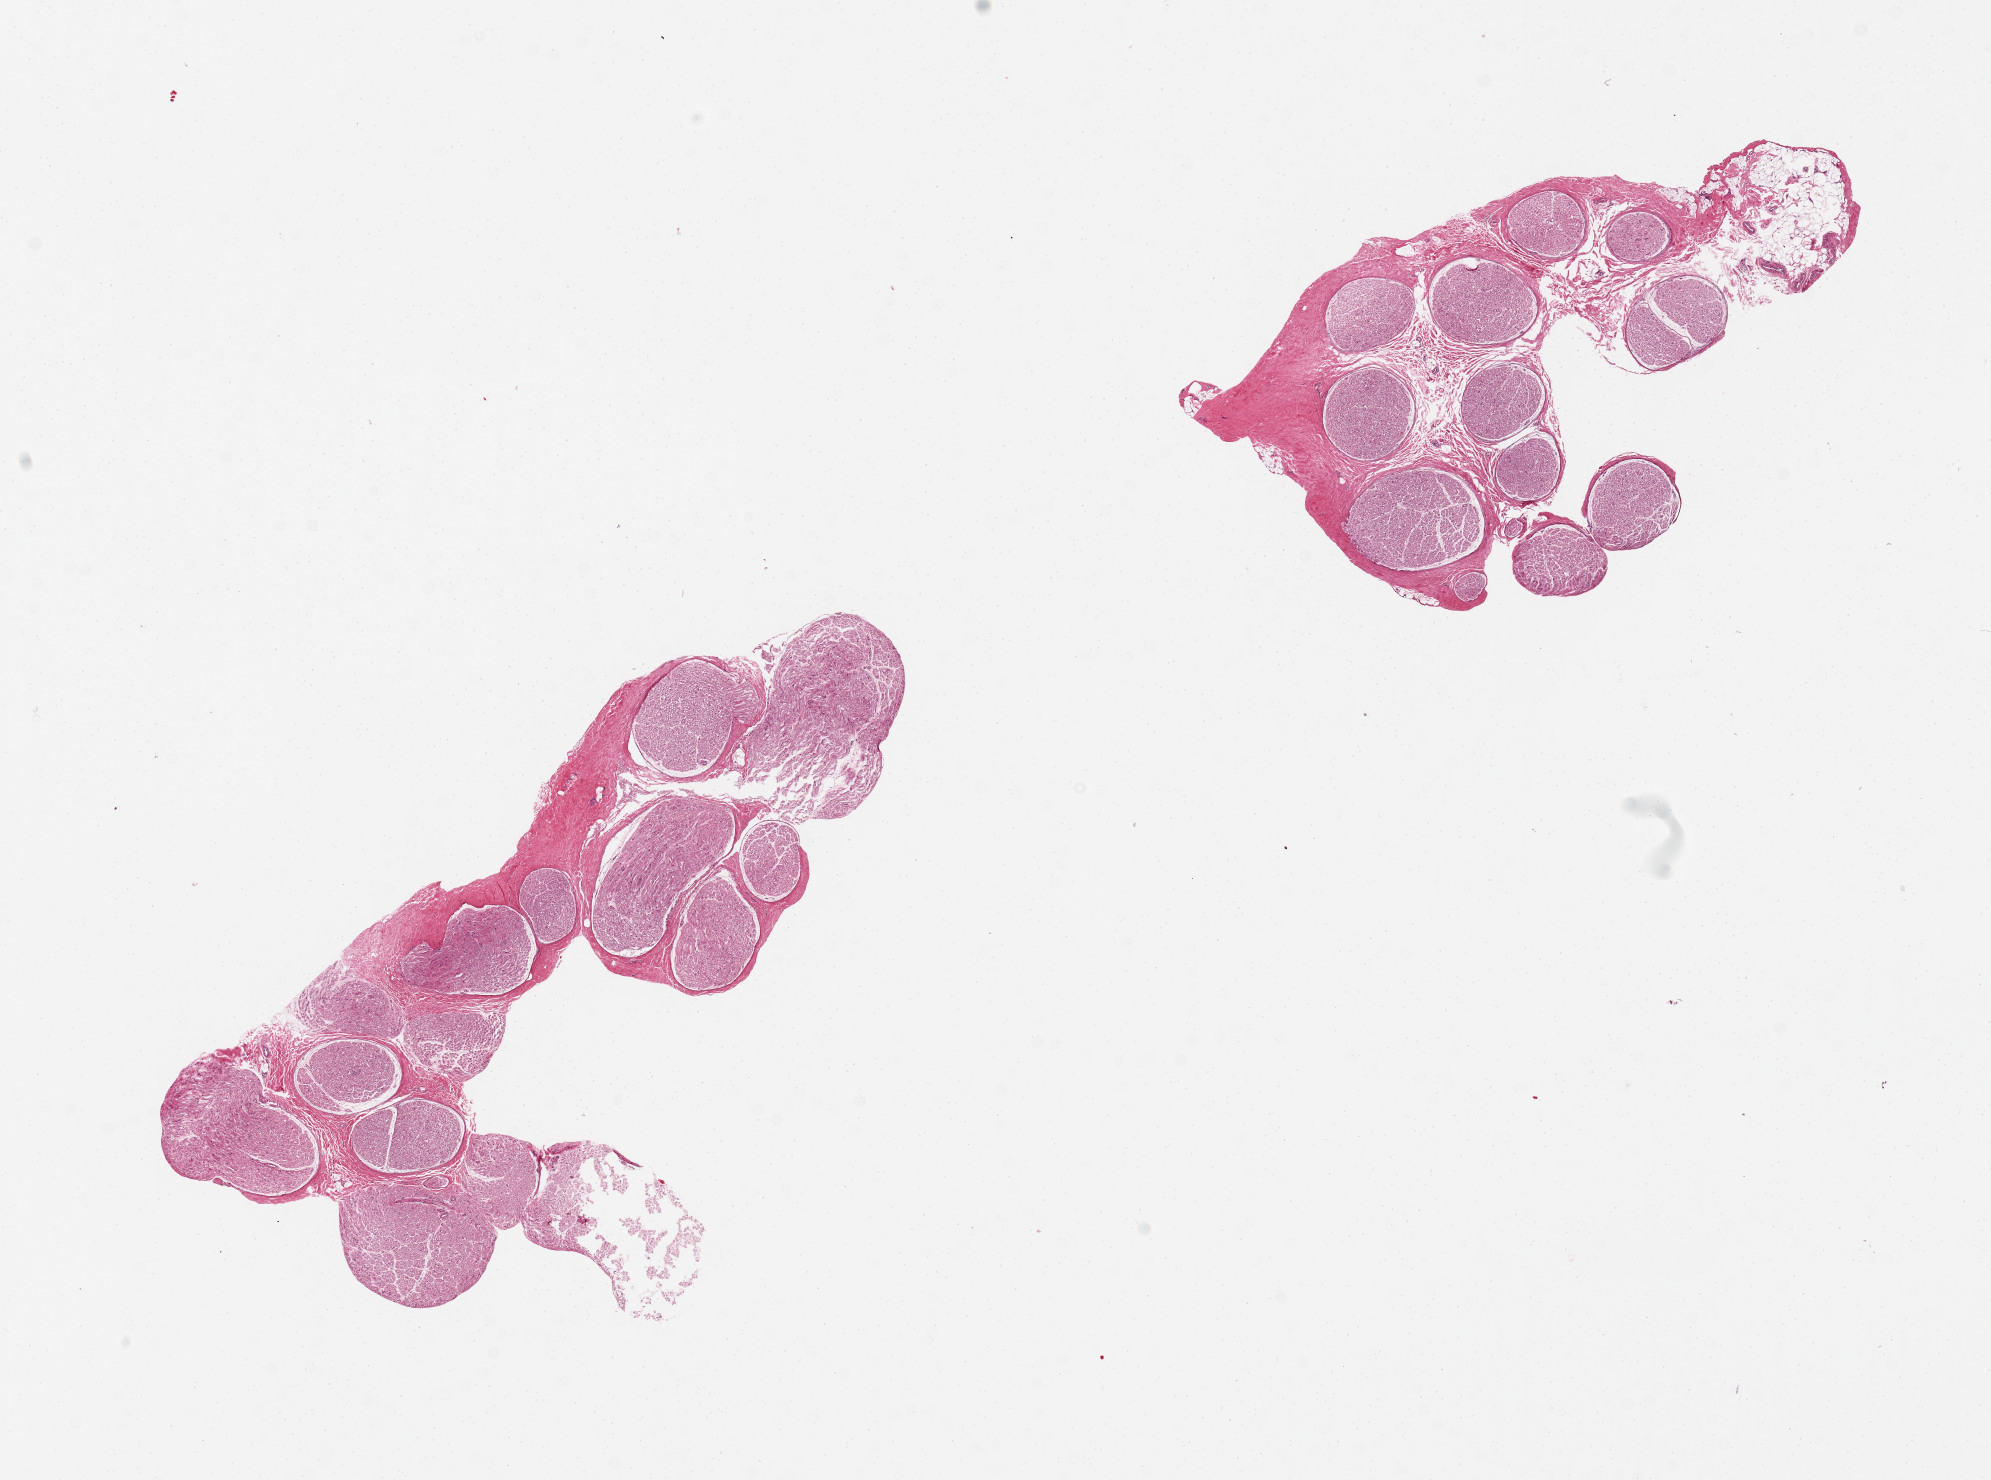
Hematoxylin and eosin (H&E) whole-slide image, brightfield, whole scanned area (about 15.8 x 11.7 mm) shown as a low-resolution overview; PAXgene-fixed, paraffin-embedded tissue; section of tibial nerve (target tissue); tissue donor sample. Male donor.
Pathologist's review note for this sample: 2 pieces; 1 mm external fat on one edge and 1.4x0.7mm dense fibrous tissue on other end.